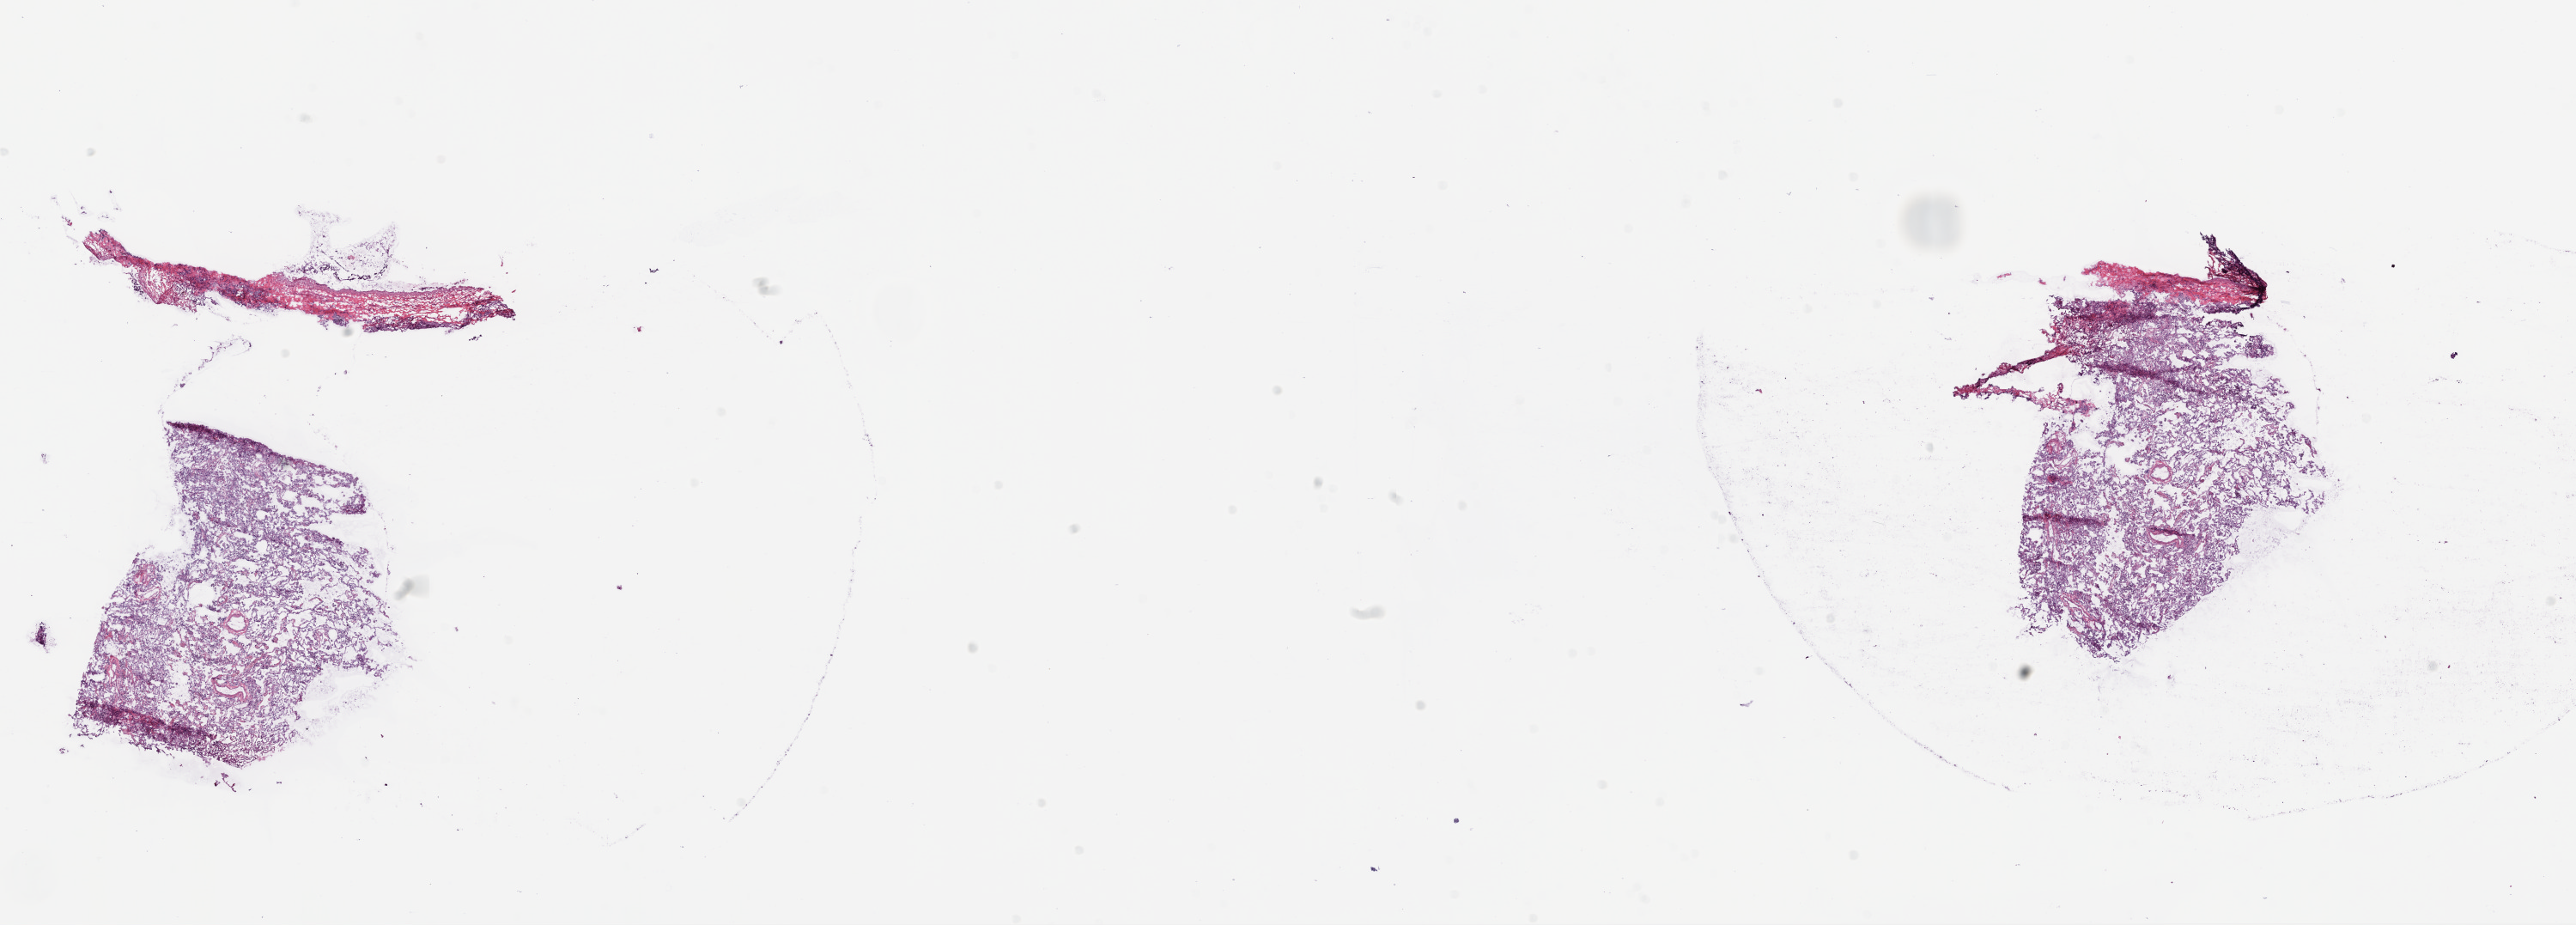
Whole-slide histology image, Hematoxylin and eosin (H&E) stained — a low-resolution overview of the entire scanned area, about 24.1 x 8.6 mm (acquisition: 20x scan); frozen section from the bottom of the tissue portion; sample: solid tissue normal (non-tumour tissue), lung. Patient: male, age at initial diagnosis 67 years.
* this section: solid tissue normal (non-tumour) sample from the same patient
* patient diagnosis: Squamous cell carcinoma, NOS (upper lobe, lung)